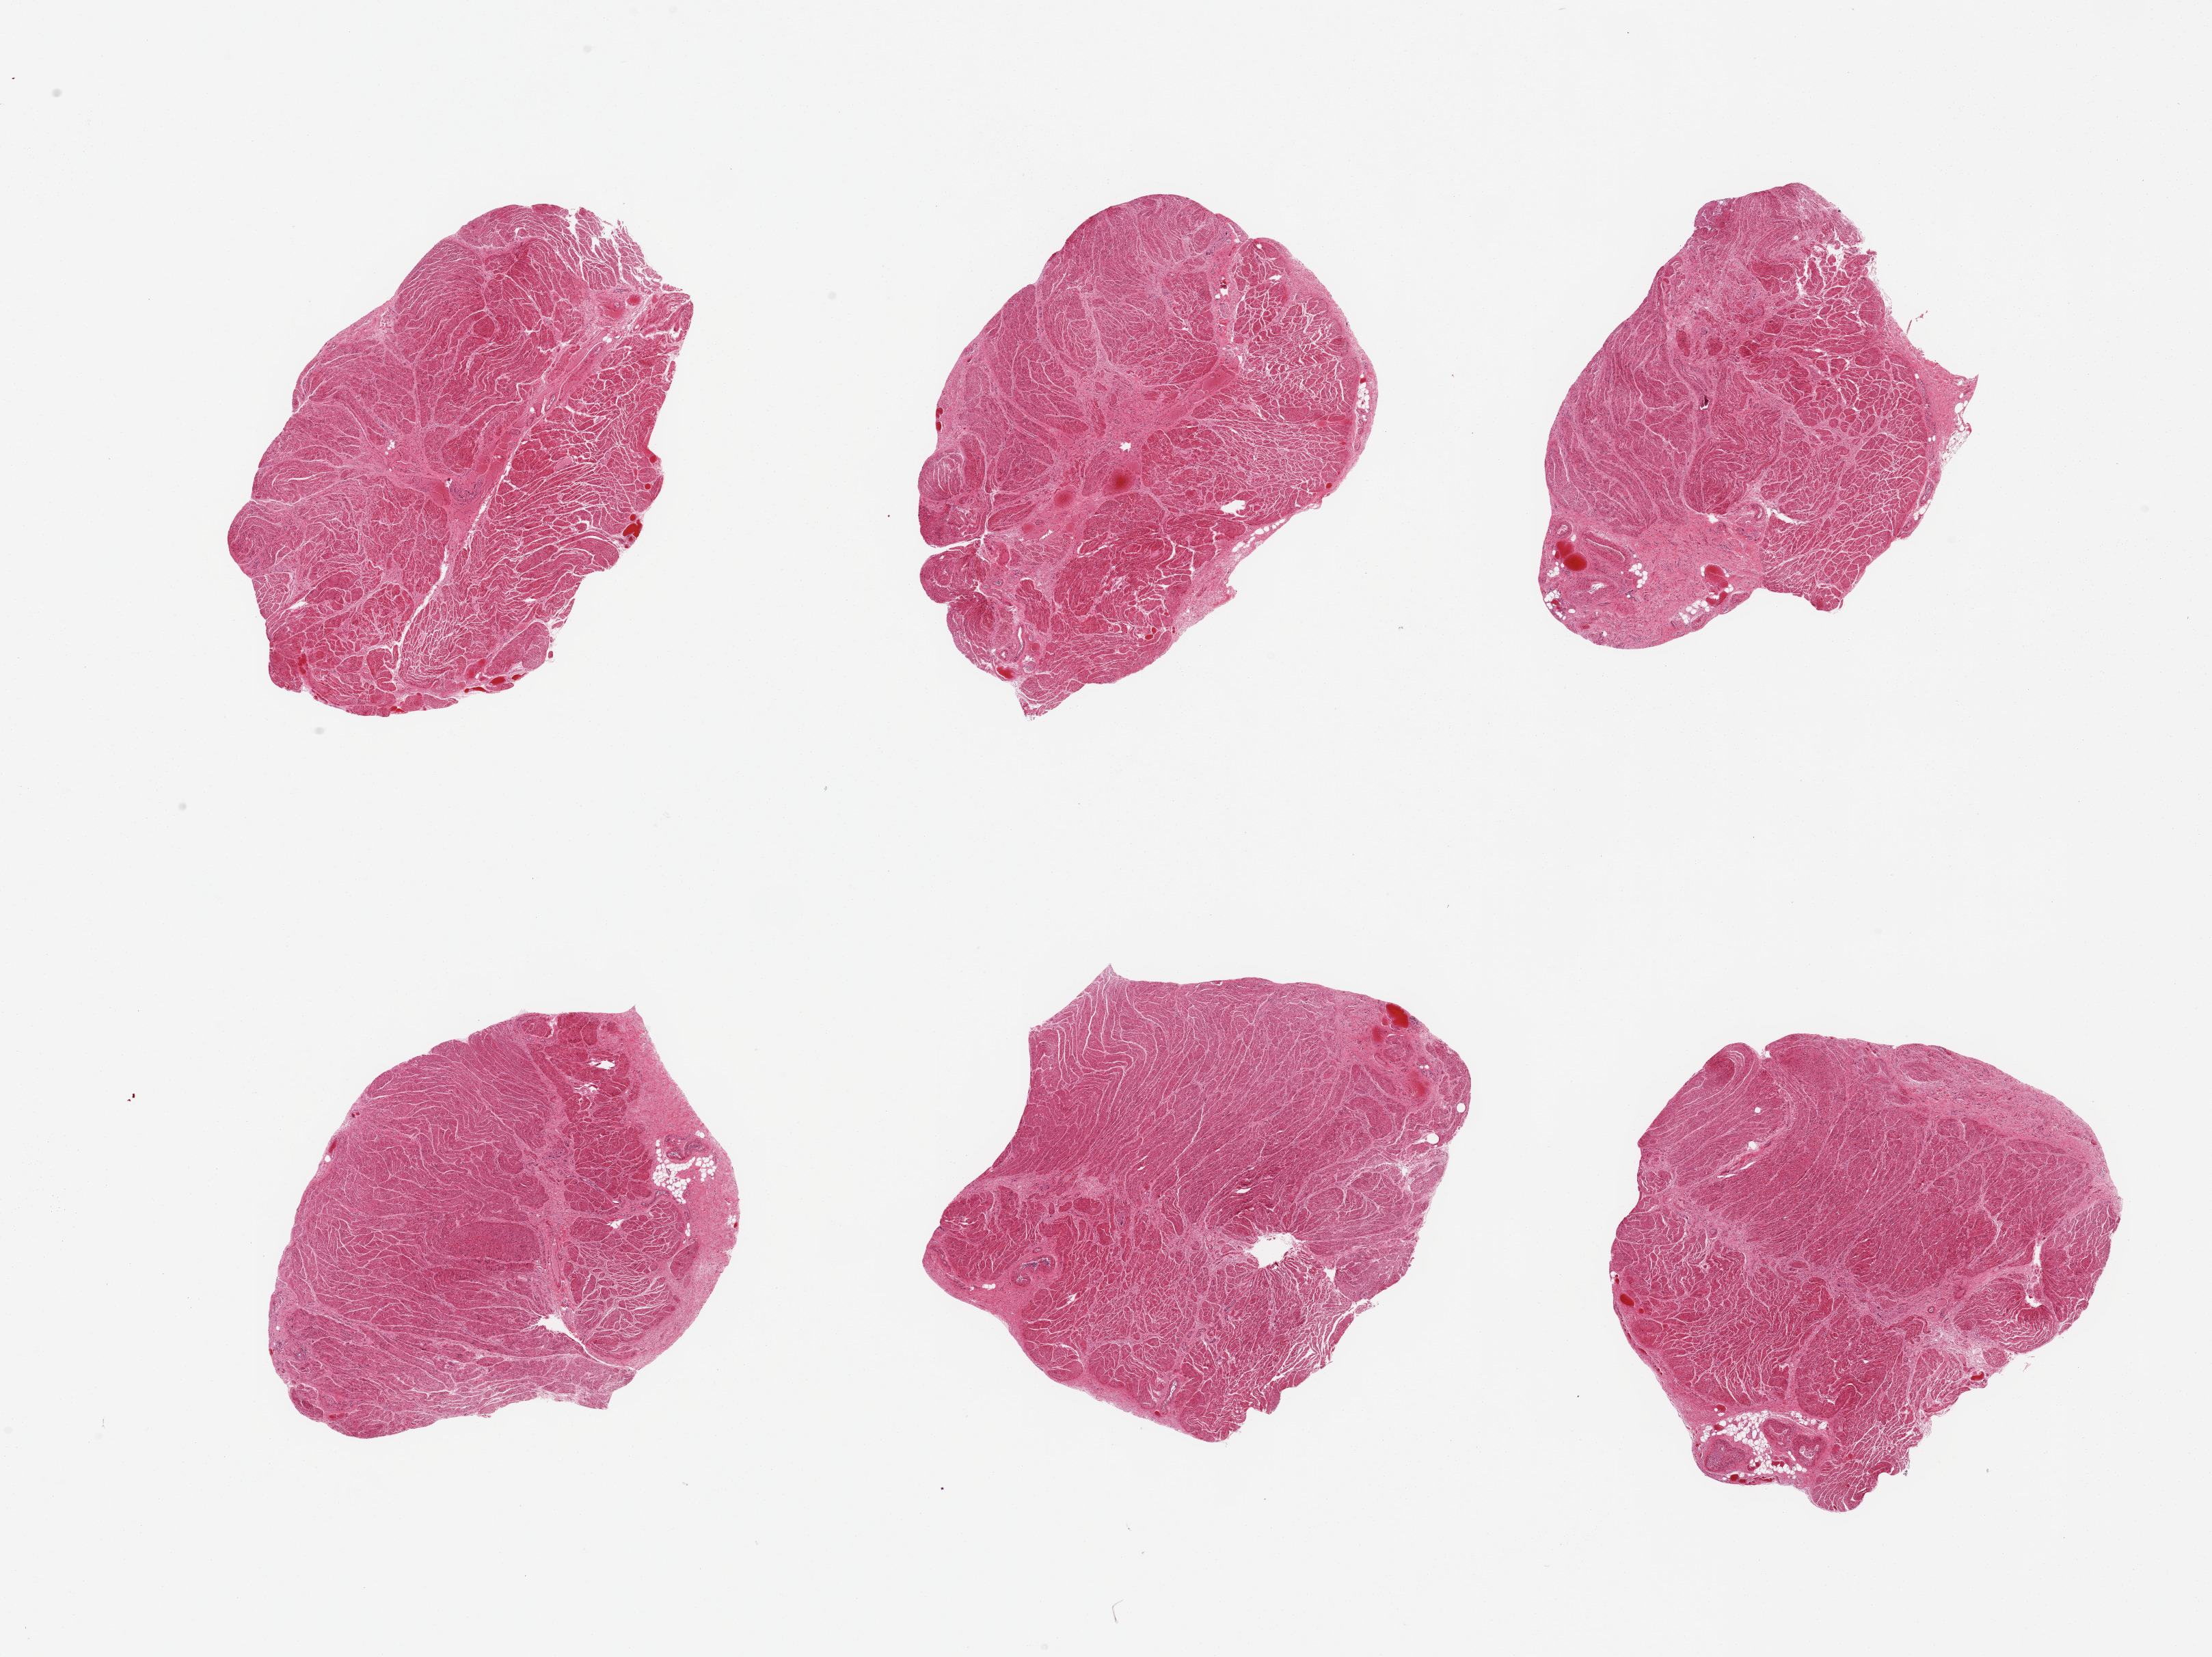
Whole-slide image, haematoxylin and eosin stain, whole scanned area (about 25.6 x 19.2 mm) shown as a low-resolution overview, PAXgene-fixed paraffin-embedded (PFPE) section, section of gastroesophageal junction (target tissue), tissue donor sample.
Review note (as recorded): 6 pieces; well trimmed target muscularis.